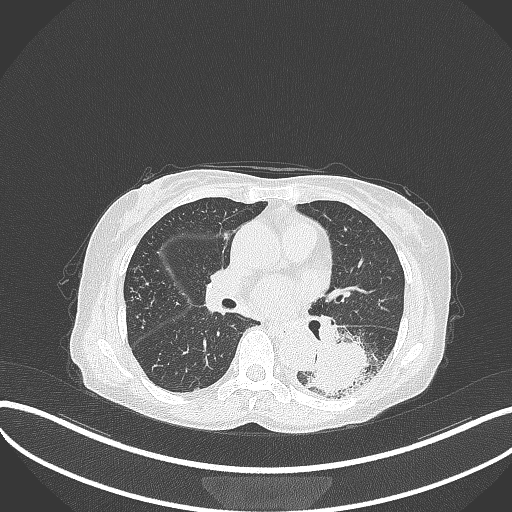
Chest CT, one axial slice; position 164 of 370 along the scan axis; lung window (W 1500 / L -600 HU); 512 × 512 image matrix. Female patient, age 78 years. Case-level facts recorded for this patient, not image findings: clinical TNM (as recorded): T3 N0 M1.
Outlined on this slice (rectangle marked by the reading radiologist):
- lung tumour (recorded histology: squamous cell carcinoma): bounding box <300,332,386,398> (left, top, right, bottom; pixels)